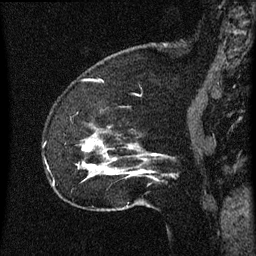
Breast MRI (dynamic contrast-enhanced), one sagittal slice. Slice 14 of 60 in the series (ordered by position). Dynamic contrast-enhanced series, image 2 of 3 at this slice position (ordered by acquisition). 1.5 T. TE 4.2 ms, TR 8 ms. 2 mm slice thickness. 256 × 256 image matrix, field of view 180 × 180 mm. Female patient, age 52 years.
Structures marked on this image (semi-automatic segmentation, software-assisted and operator-edited):
- analysis volume of interest (the breast-tissue region the enhancement analysis was run in; not a lesion): bounding box <54,124,166,207> (left, top, right, bottom; pixels)
- tumour enhancement mask (voxels above the 70 % enhancement threshold inside the analysis volume of interest): <78,148,158,175>